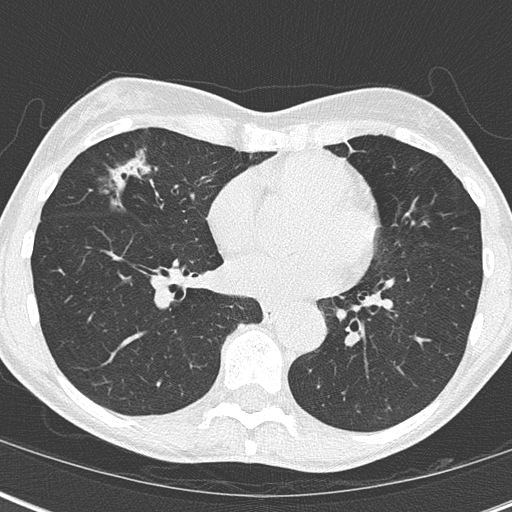
Chest CT (low-dose screening protocol), one axial image, third screening round (two years after baseline), lung window (W 1500 / L -600 HU), 2 mm slice thickness, 120 kVp. Female, age 67 years at enrolment. Current smoker at enrolment.
Lesion marked by an expert reader, bounding box [x1, y1, x2, y2] px = [94, 144, 194, 236]. Screening reader's record for this exam (one nodule recorded; not confirmed to be the boxed lesion): non-calcified nodule or mass ≥4 mm, right middle lobe, 32 × 17 mm, mixed attenuation, pre-existing on the prior screen: yes; interval growth: yes. Official screen result: positive, other. Participant outcome: lung cancer diagnosed 76 days after this screen — bronchiolo-alveolar adenocarcinoma, NOS, right middle lobe, well differentiated (G1), stage IA (AJCC 6th edition), 25 mm at pathology.